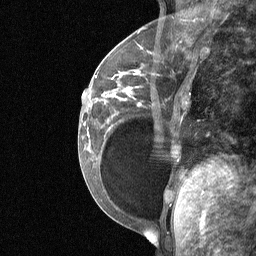
Breast MRI (dynamic contrast-enhanced), one sagittal slice; slice 22 of 64 in the series (ordered by position); dynamic contrast-enhanced study with each time point stored as its own series, time point 2 of 3 at this slice position (early post-contrast, ordered by acquisition time); 1.5 T; TE 4.8 ms, TR 27 ms; 2 mm slice thickness; 256 × 256 image matrix. Female patient, age 34 years. Case-level facts recorded for this patient, not image findings: setting: breast cancer imaged before/during neoadjuvant chemotherapy; receptor status: HR-positive, HER2-negative.
Structures marked on this image (semi-automatic segmentation, software-assisted and operator-edited):
- analysis volume of interest (the breast-tissue region the enhancement analysis was run in; not a lesion): bounding box [x1, y1, x2, y2] px = [92, 50, 188, 185]
- tumour enhancement mask (voxels above the 90 % enhancement threshold inside the analysis volume of interest): [129, 72, 138, 89]